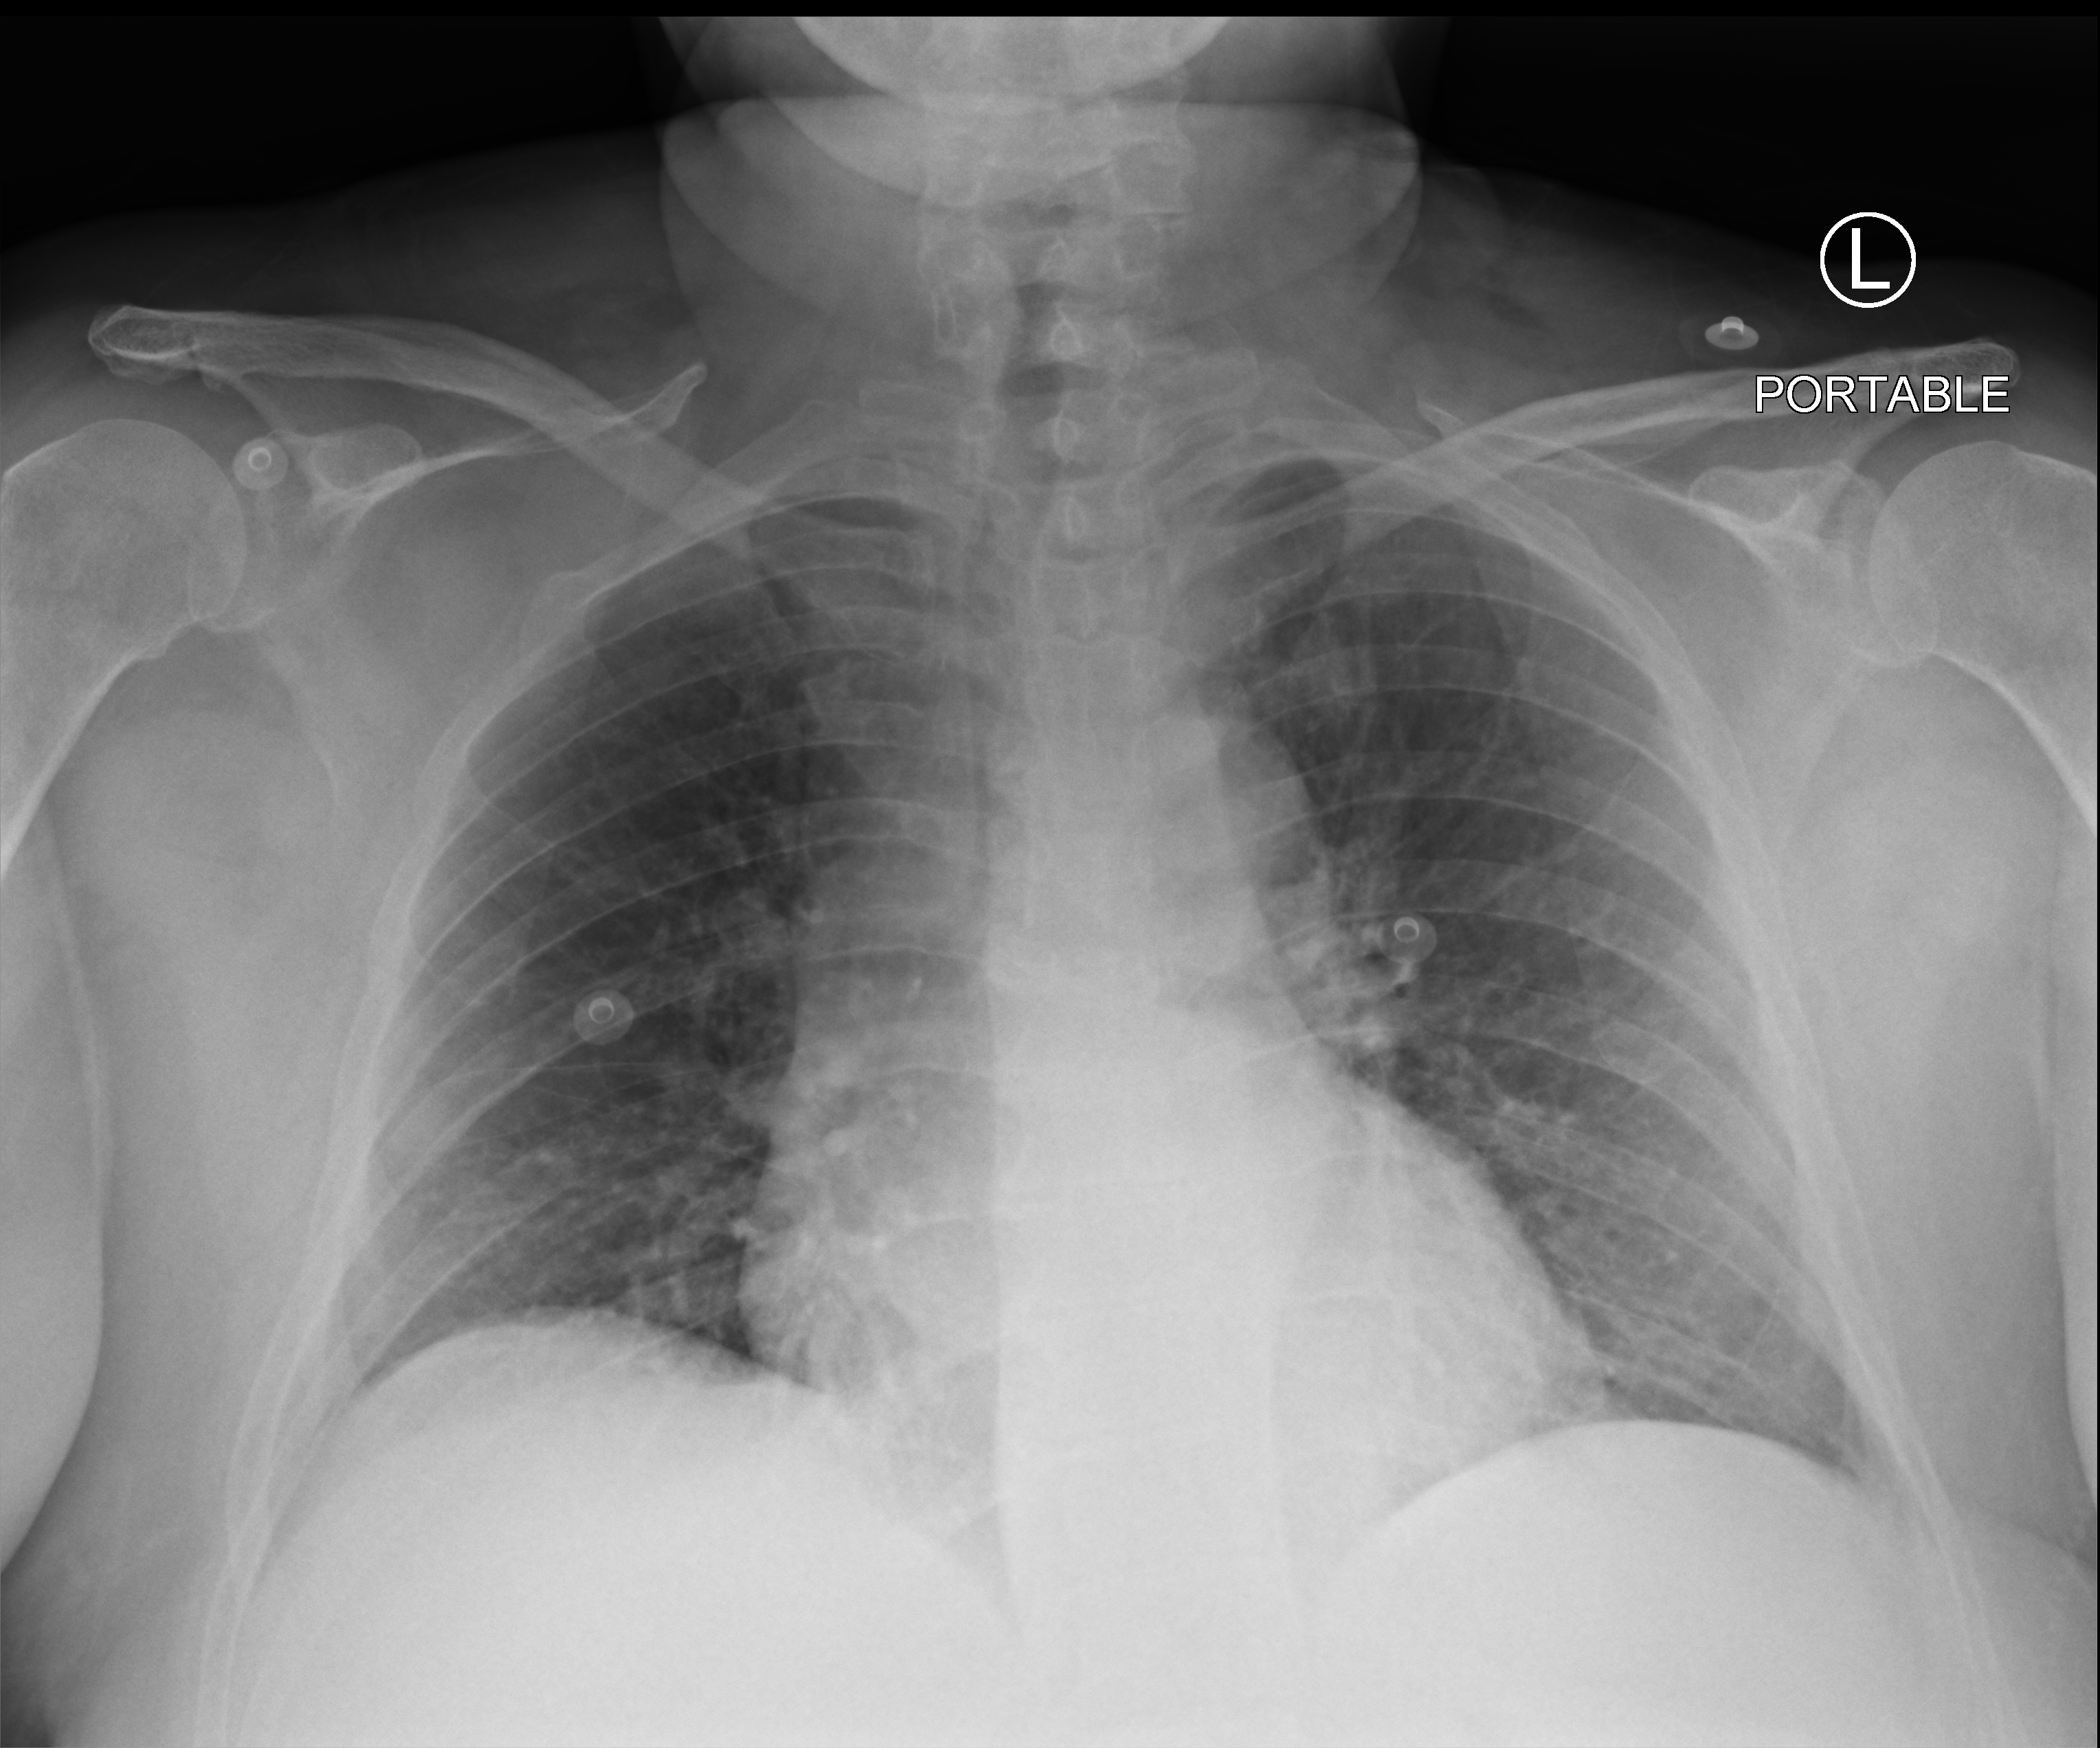
Portable chest radiograph, anteroposterior (AP) projection. Patient hospitalised with COVID-19; female, aged 60–74 years.
Hospital-stay facts (about this admission, not read from this image; timing relative to this image not recorded): length of hospital stay: 2 days; diabetes (admission record): yes.